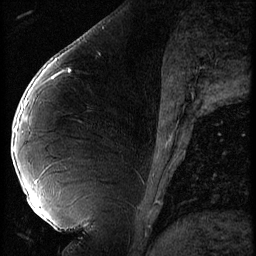
Breast MRI (dynamic contrast-enhanced), one sagittal slice; position 22 of 56 along the scan axis; 3 images stored at this slice position (order not interpretable as contrast timing); 1.5 T; TE 4.2 ms, TR 9 ms; 2.5 mm slice thickness; 256 × 256 image matrix. Female patient, age 43 years. Case-level facts recorded for this patient, not image findings: setting: breast cancer imaged before/during neoadjuvant chemotherapy; receptor status: HER2-positive.
Outlined on this slice (semi-automatically segmented with operator editing):
- analysis volume of interest (the breast-tissue region the enhancement analysis was run in; not a lesion): box from (x=12, y=92) to (x=74, y=211) px
- tumour enhancement mask (voxels above the 140 % enhancement threshold inside the analysis volume of interest): (x=16, y=129)–(x=18, y=131)